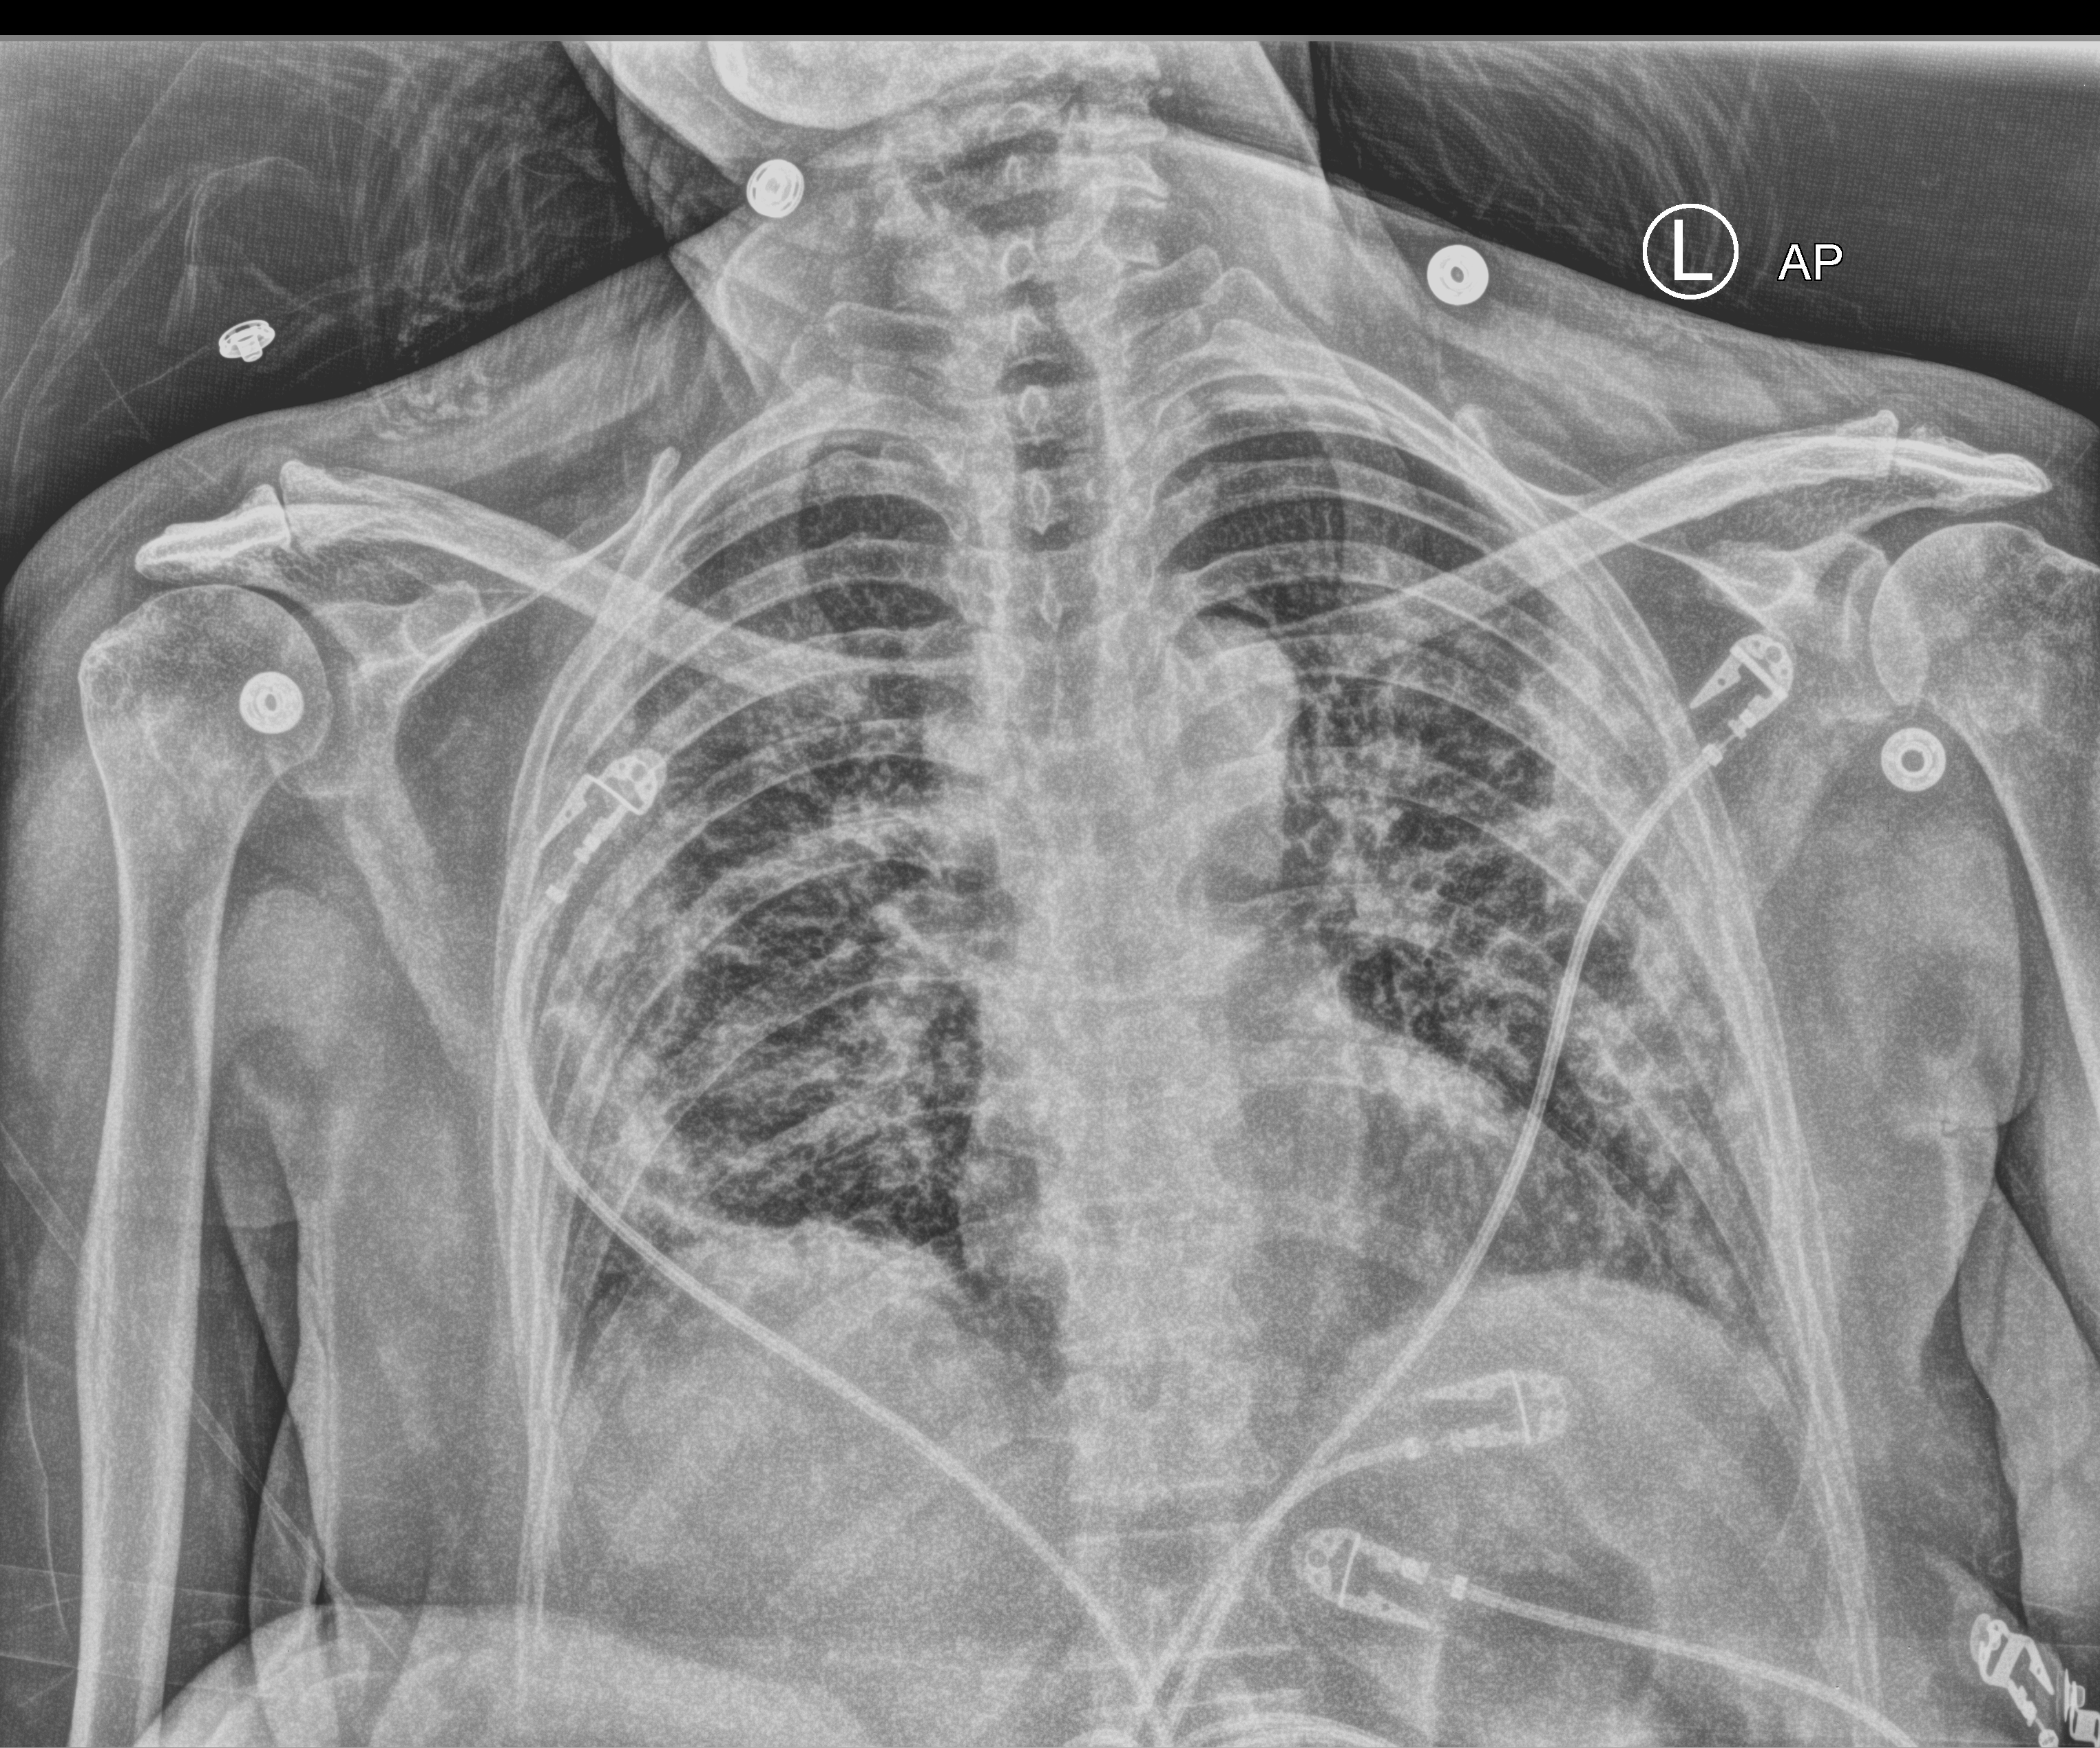
Portable chest radiograph; anteroposterior (AP) projection. Female patient hospitalised with COVID-19, age 60–74 years.
Hospital-stay facts (about this admission, not read from this image; timing relative to this image not recorded):
- chronic kidney disease (admission record): no
- admitted to intensive care during this hospital stay: yes
- mechanically ventilated during this hospital stay: yes